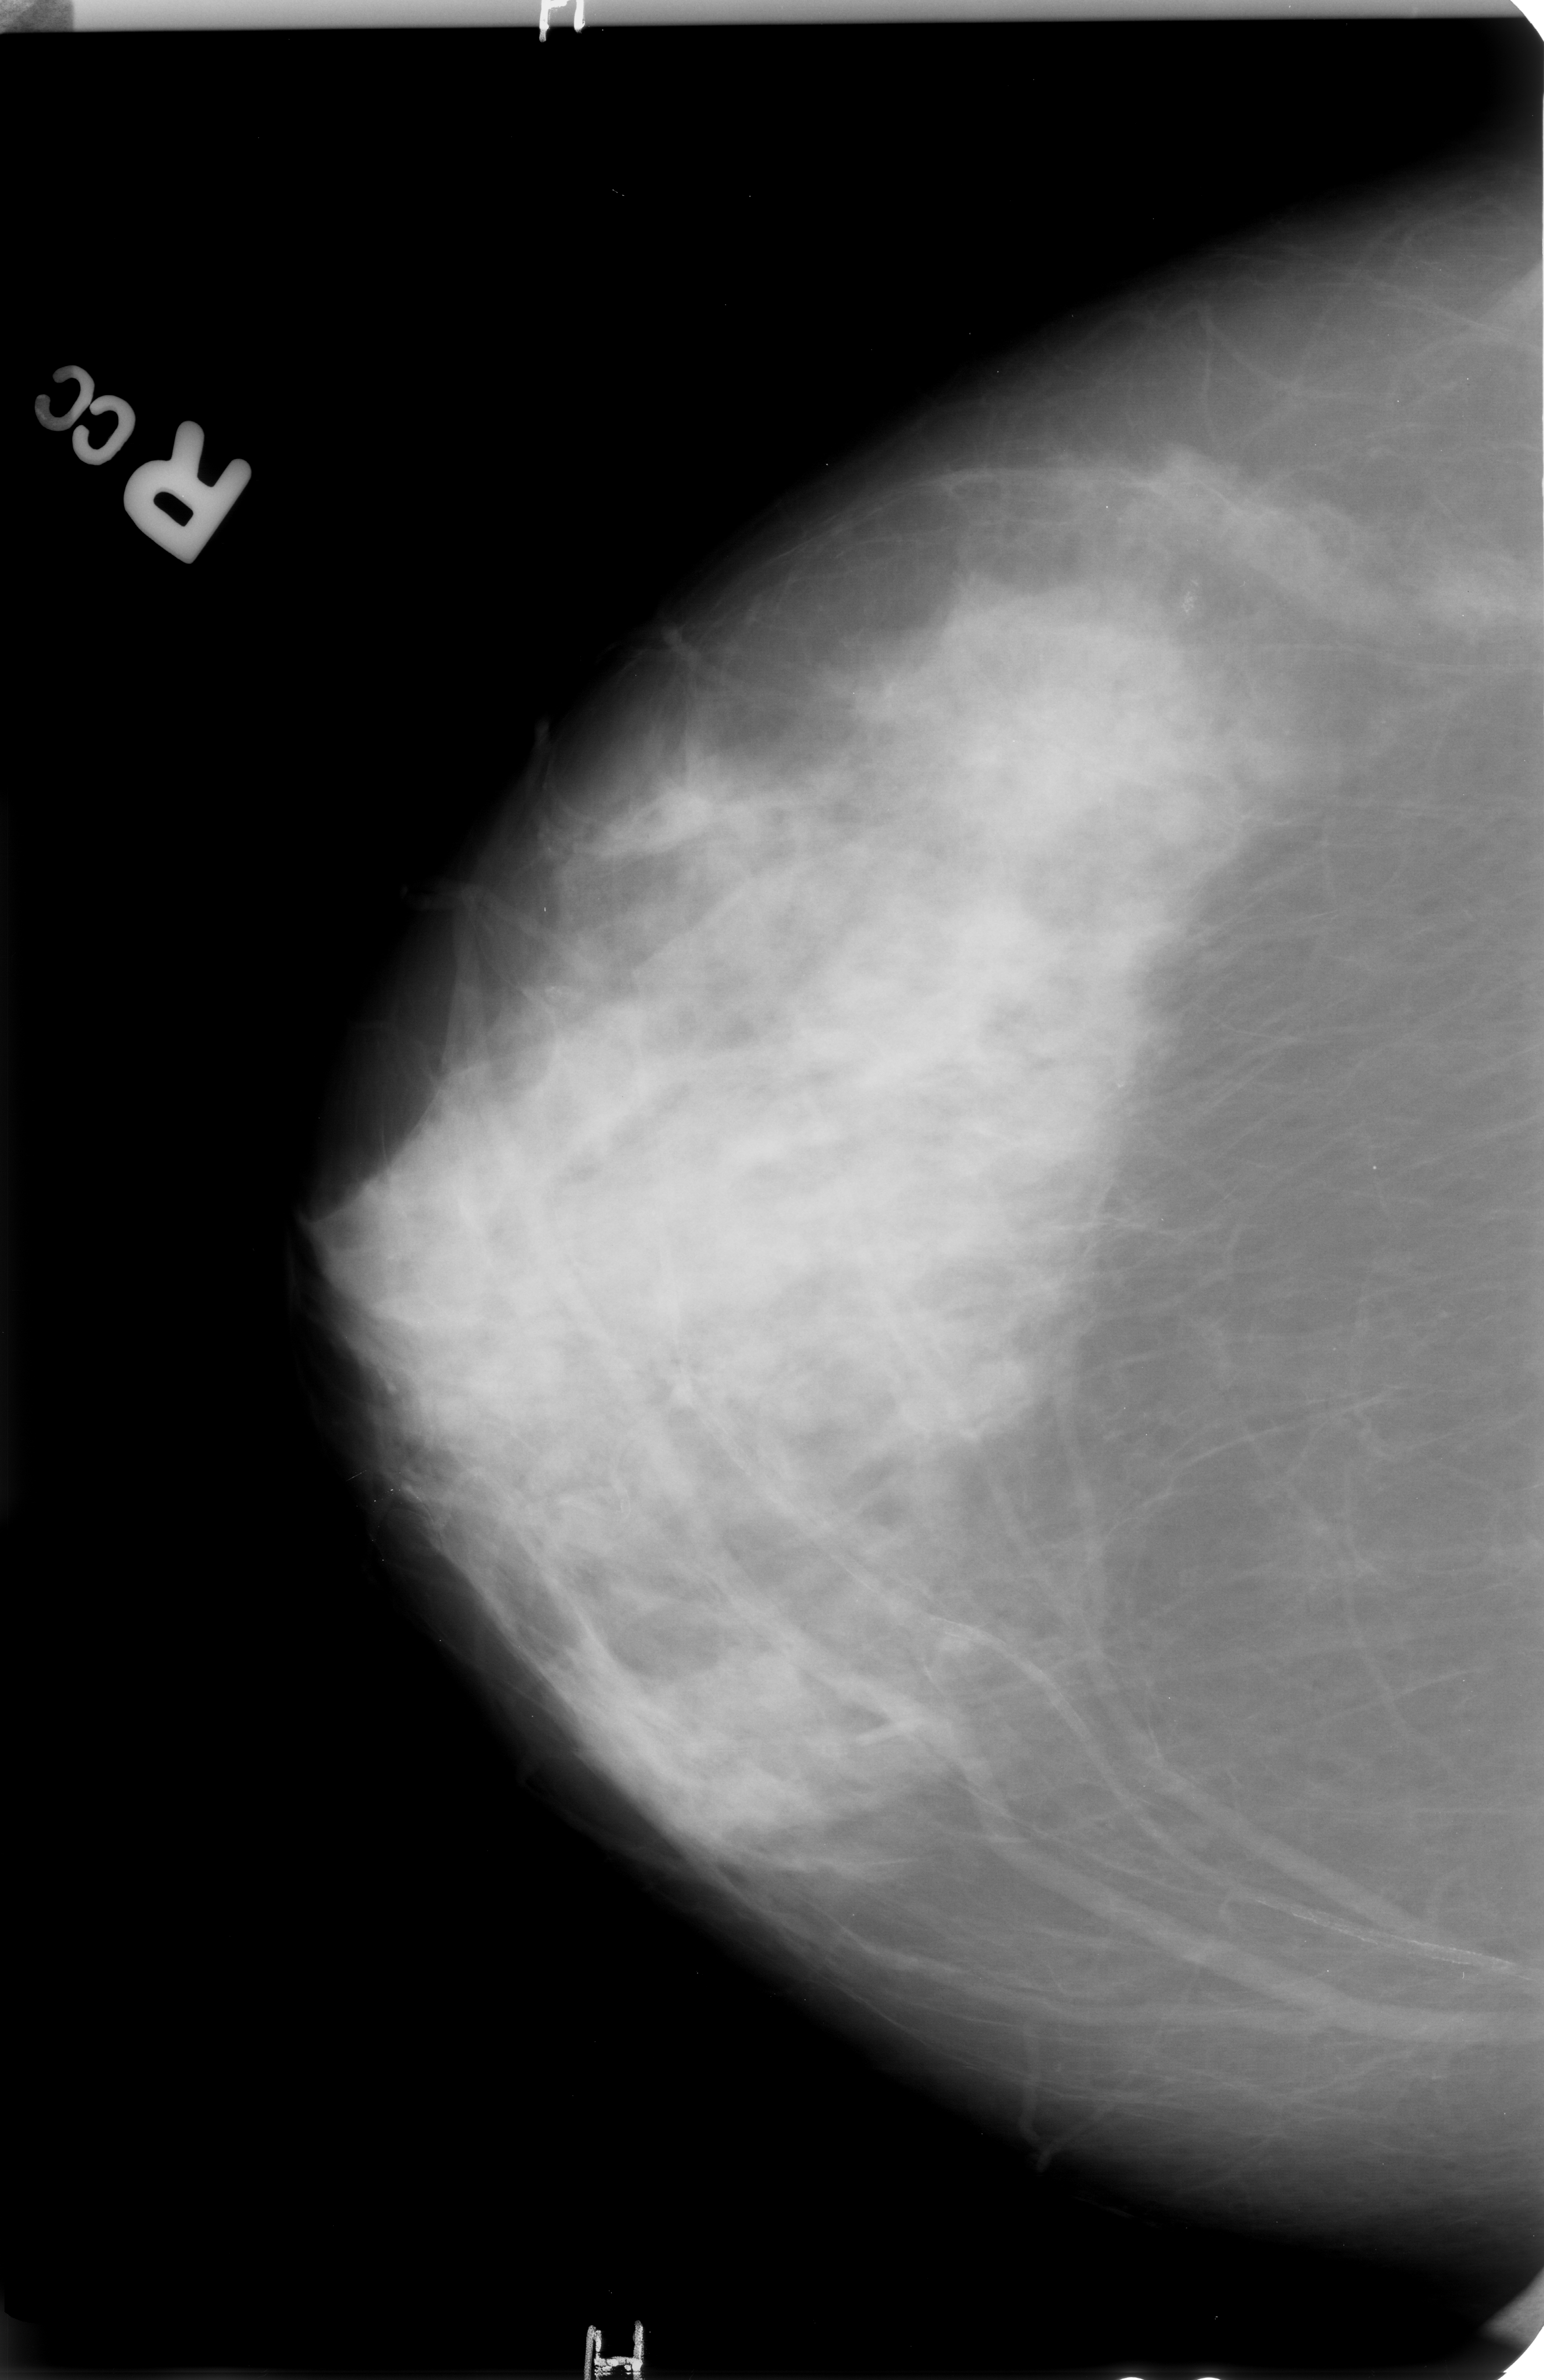
Scanned film-screen mammogram; right breast; craniocaudal (CC) view; BI-RADS breast density category 3 (scale 1–4).
Abnormality record for this image: calcifications, morphology pleomorphic, distribution clustered; BI-RADS assessment category 4; pathology result (as recorded, not read from the image): benign.